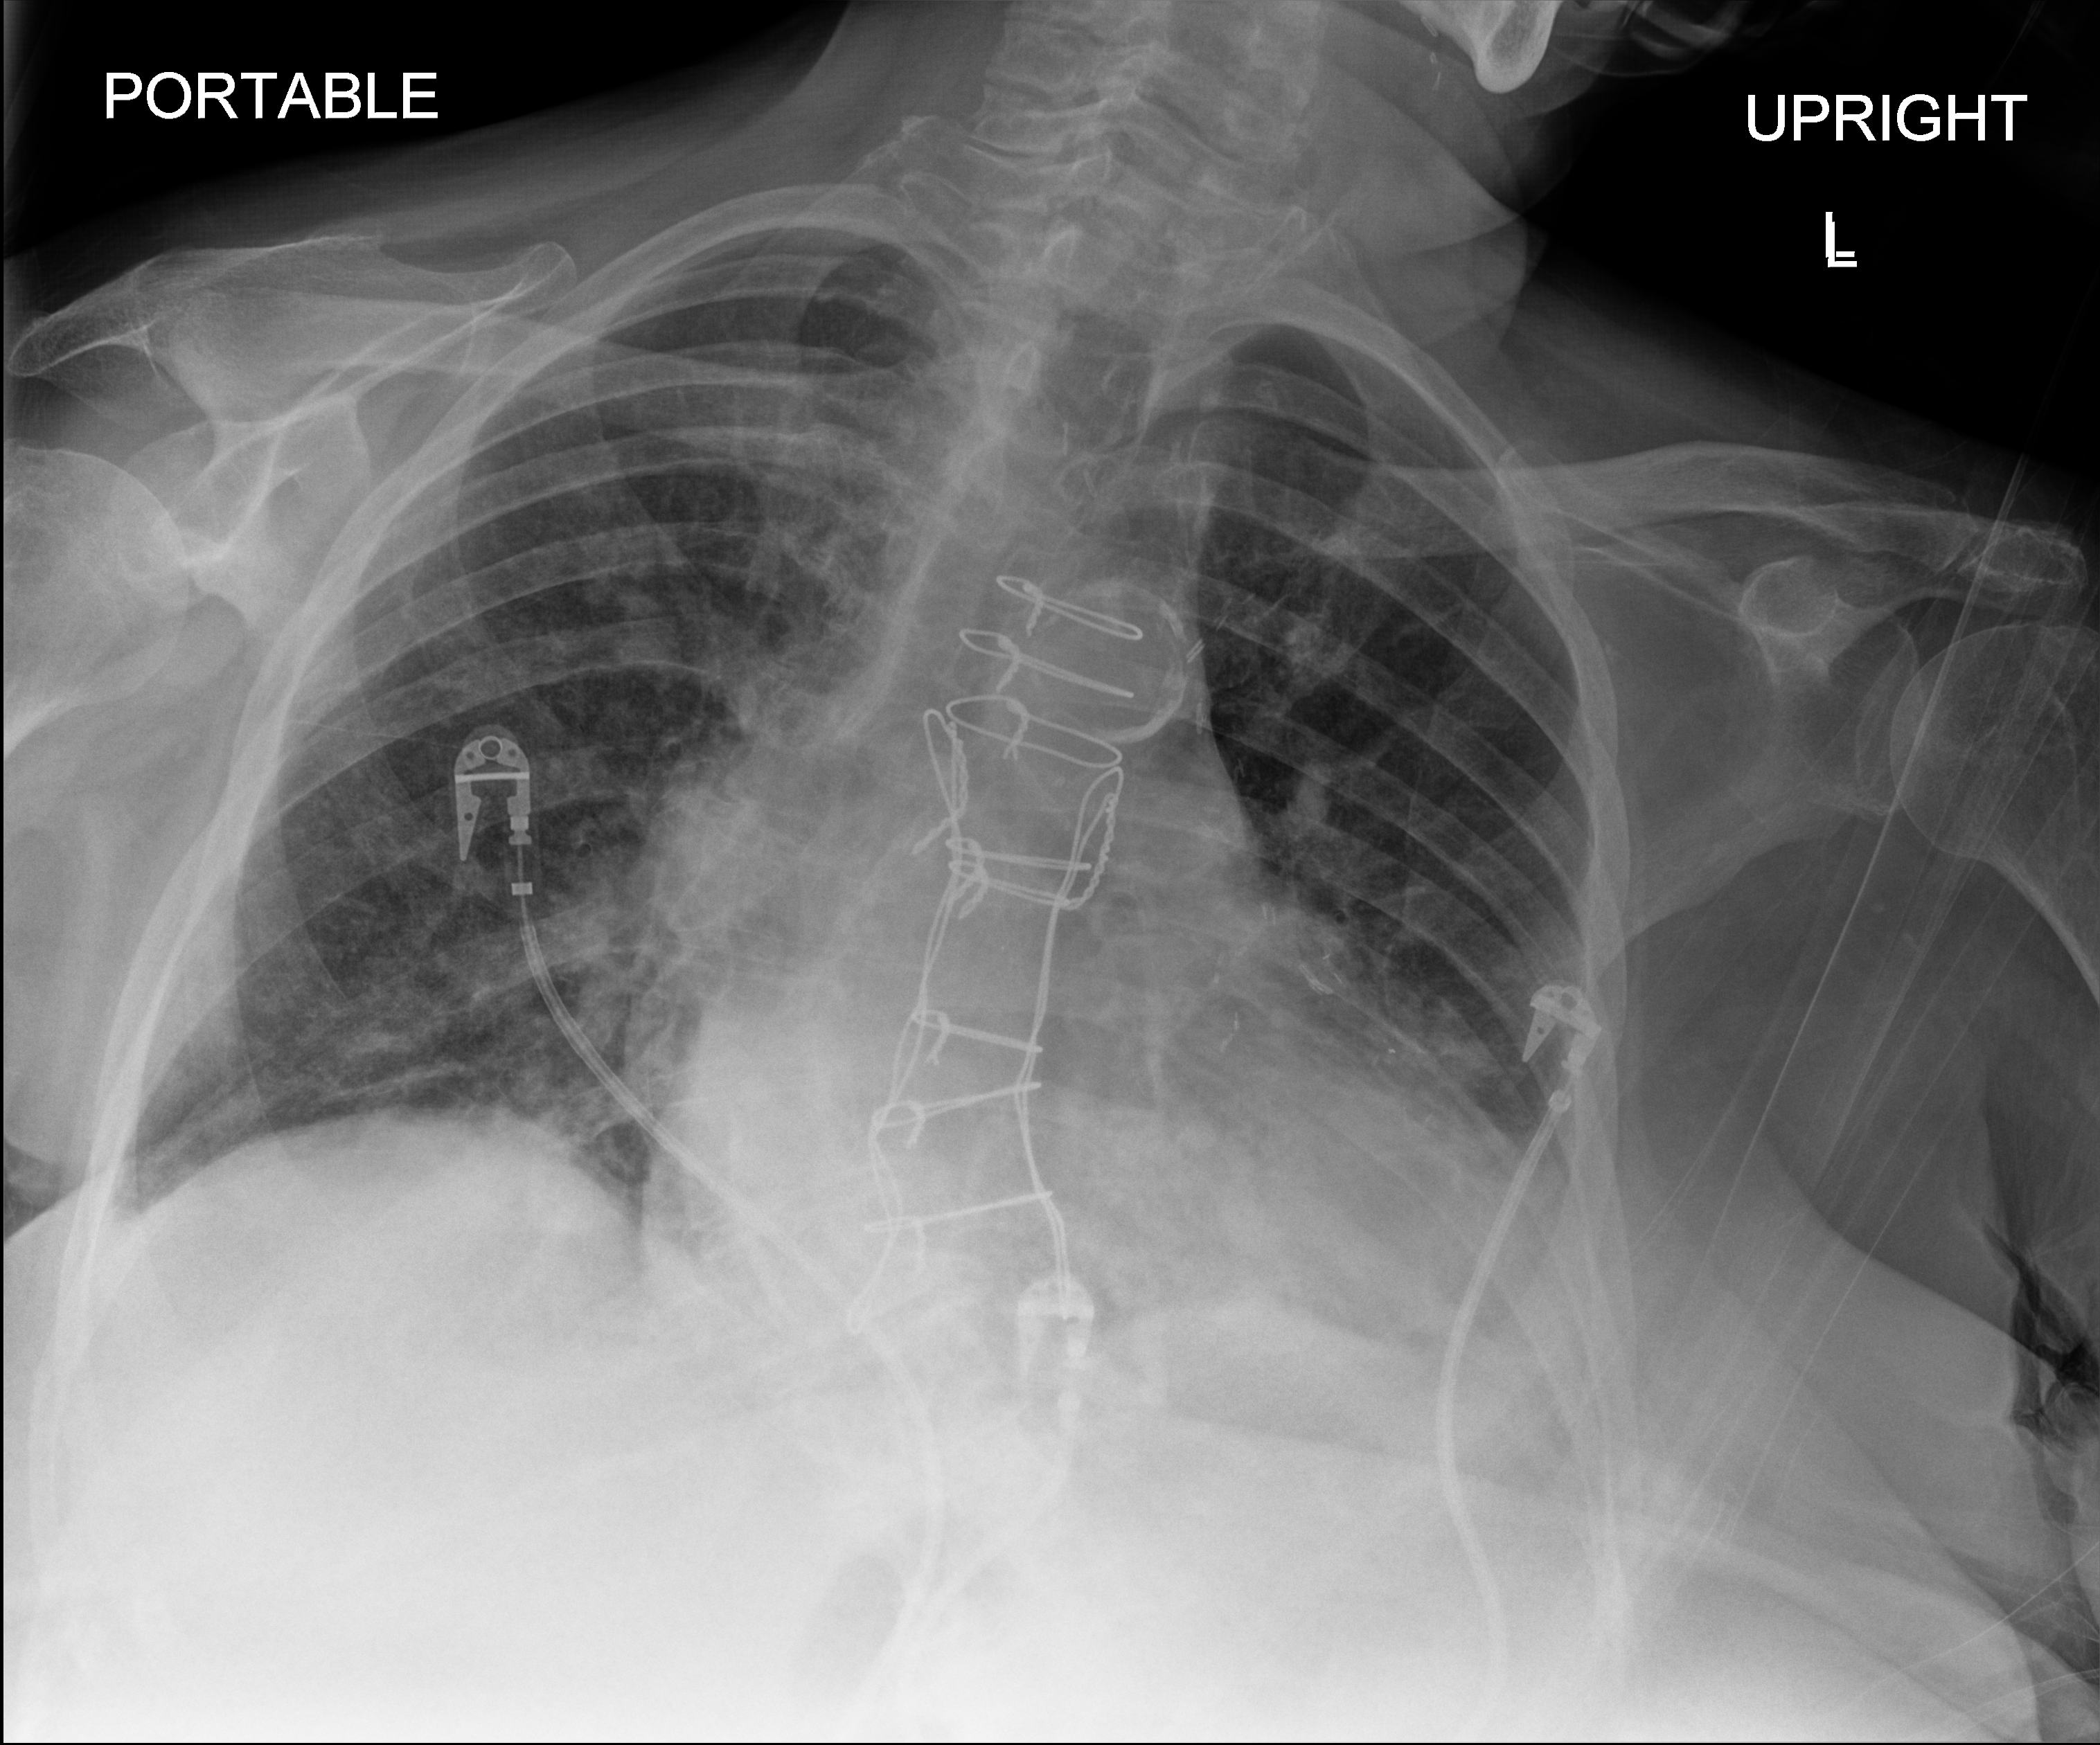
Chest X-ray (portable), anteroposterior (AP) projection. Female patient hospitalised with COVID-19, age 75–90 years.
Admission-level facts for this patient (not findings on this image; timing relative to this image not recorded):
- length of hospital stay: 10 days
- mechanically ventilated during this hospital stay: no
- admitted to intensive care during this hospital stay: no